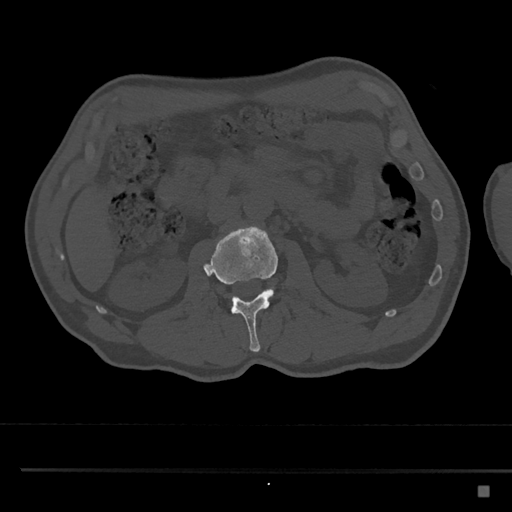
CT including the spine, one axial slice. Position 749 of 797 along the scan axis. 120 kVp. Bone window (W 1800 / L 400 HU). 512 × 512 image matrix, field of view 391 × 391 mm. Male patient, age 59 years. From the clinical record (not read from this slice): primary cancer: prostate.
Outlined on this slice (semi-automatic segmentation, software-assisted and operator-edited):
- L2 vertebra: bounding box <203,226,278,352> (left, top, right, bottom; pixels)